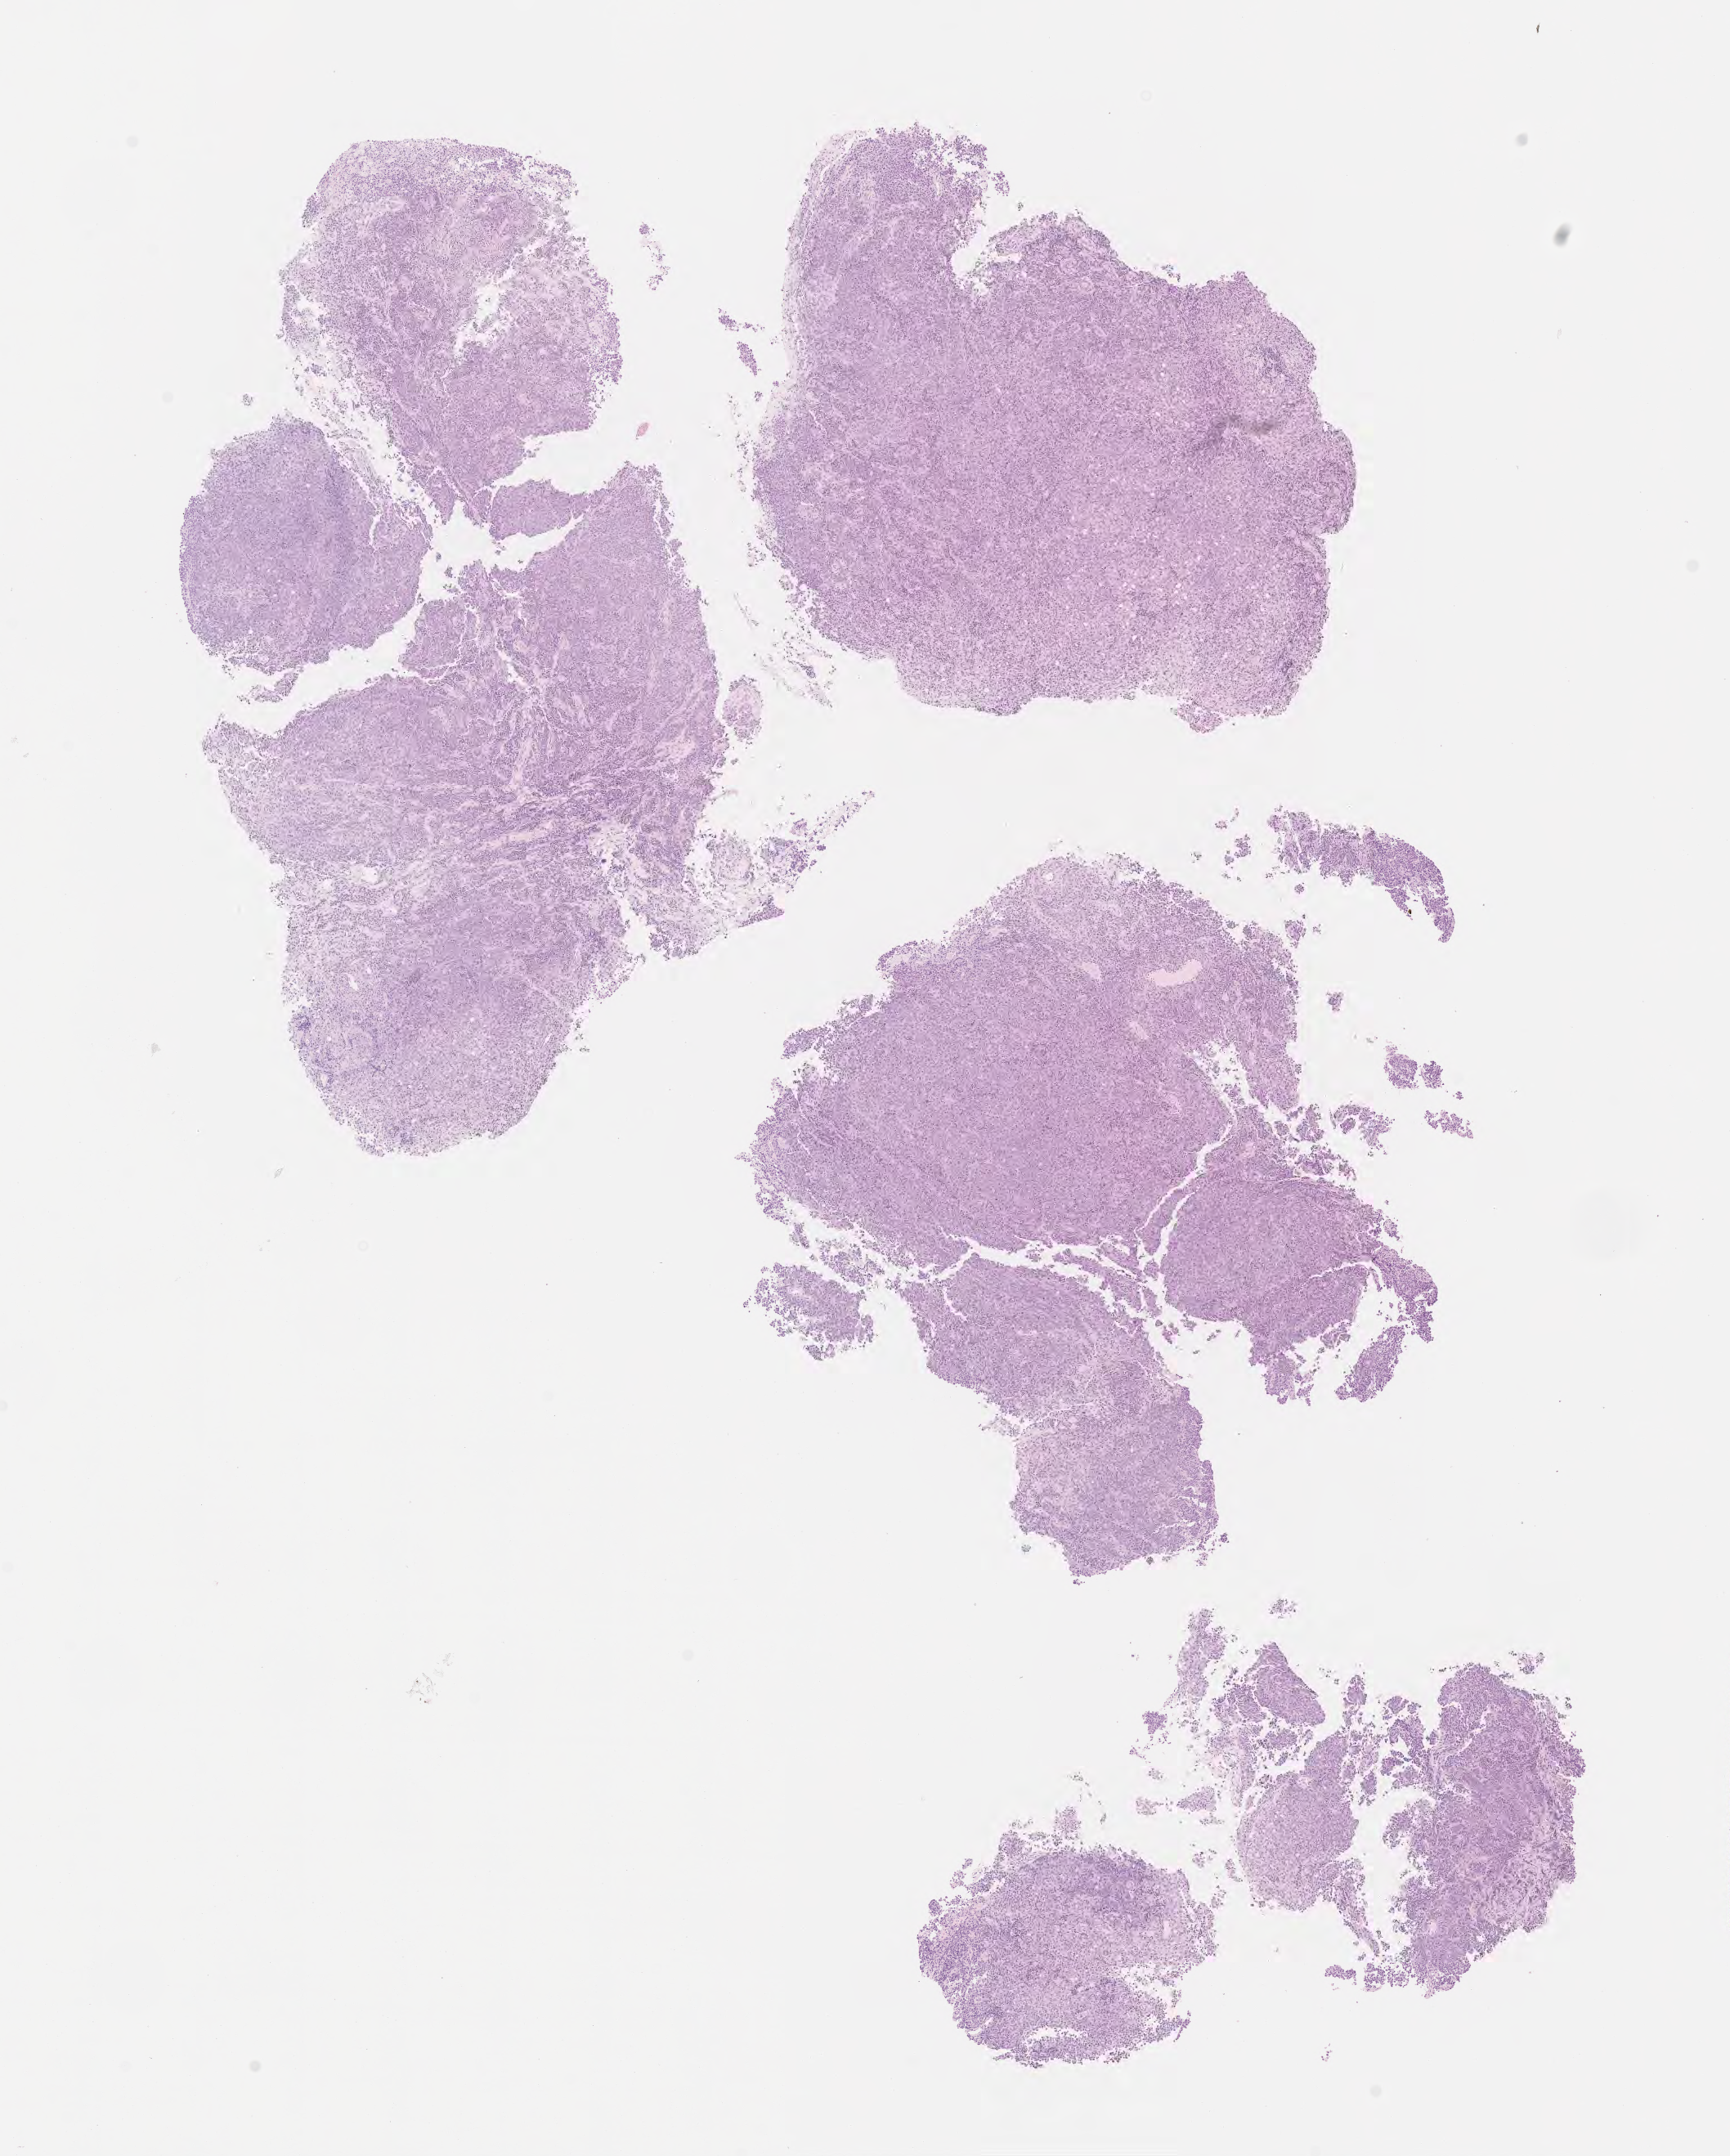
Digitized H&E-stained section, shown as a low-resolution overview of the whole scanned area (about 8.6 x 10.7 mm). Specimen: tumor tissue. Site: cervix. Patient female; 75 years old.
Diagnosis: Adenocarcinoma, NOS.